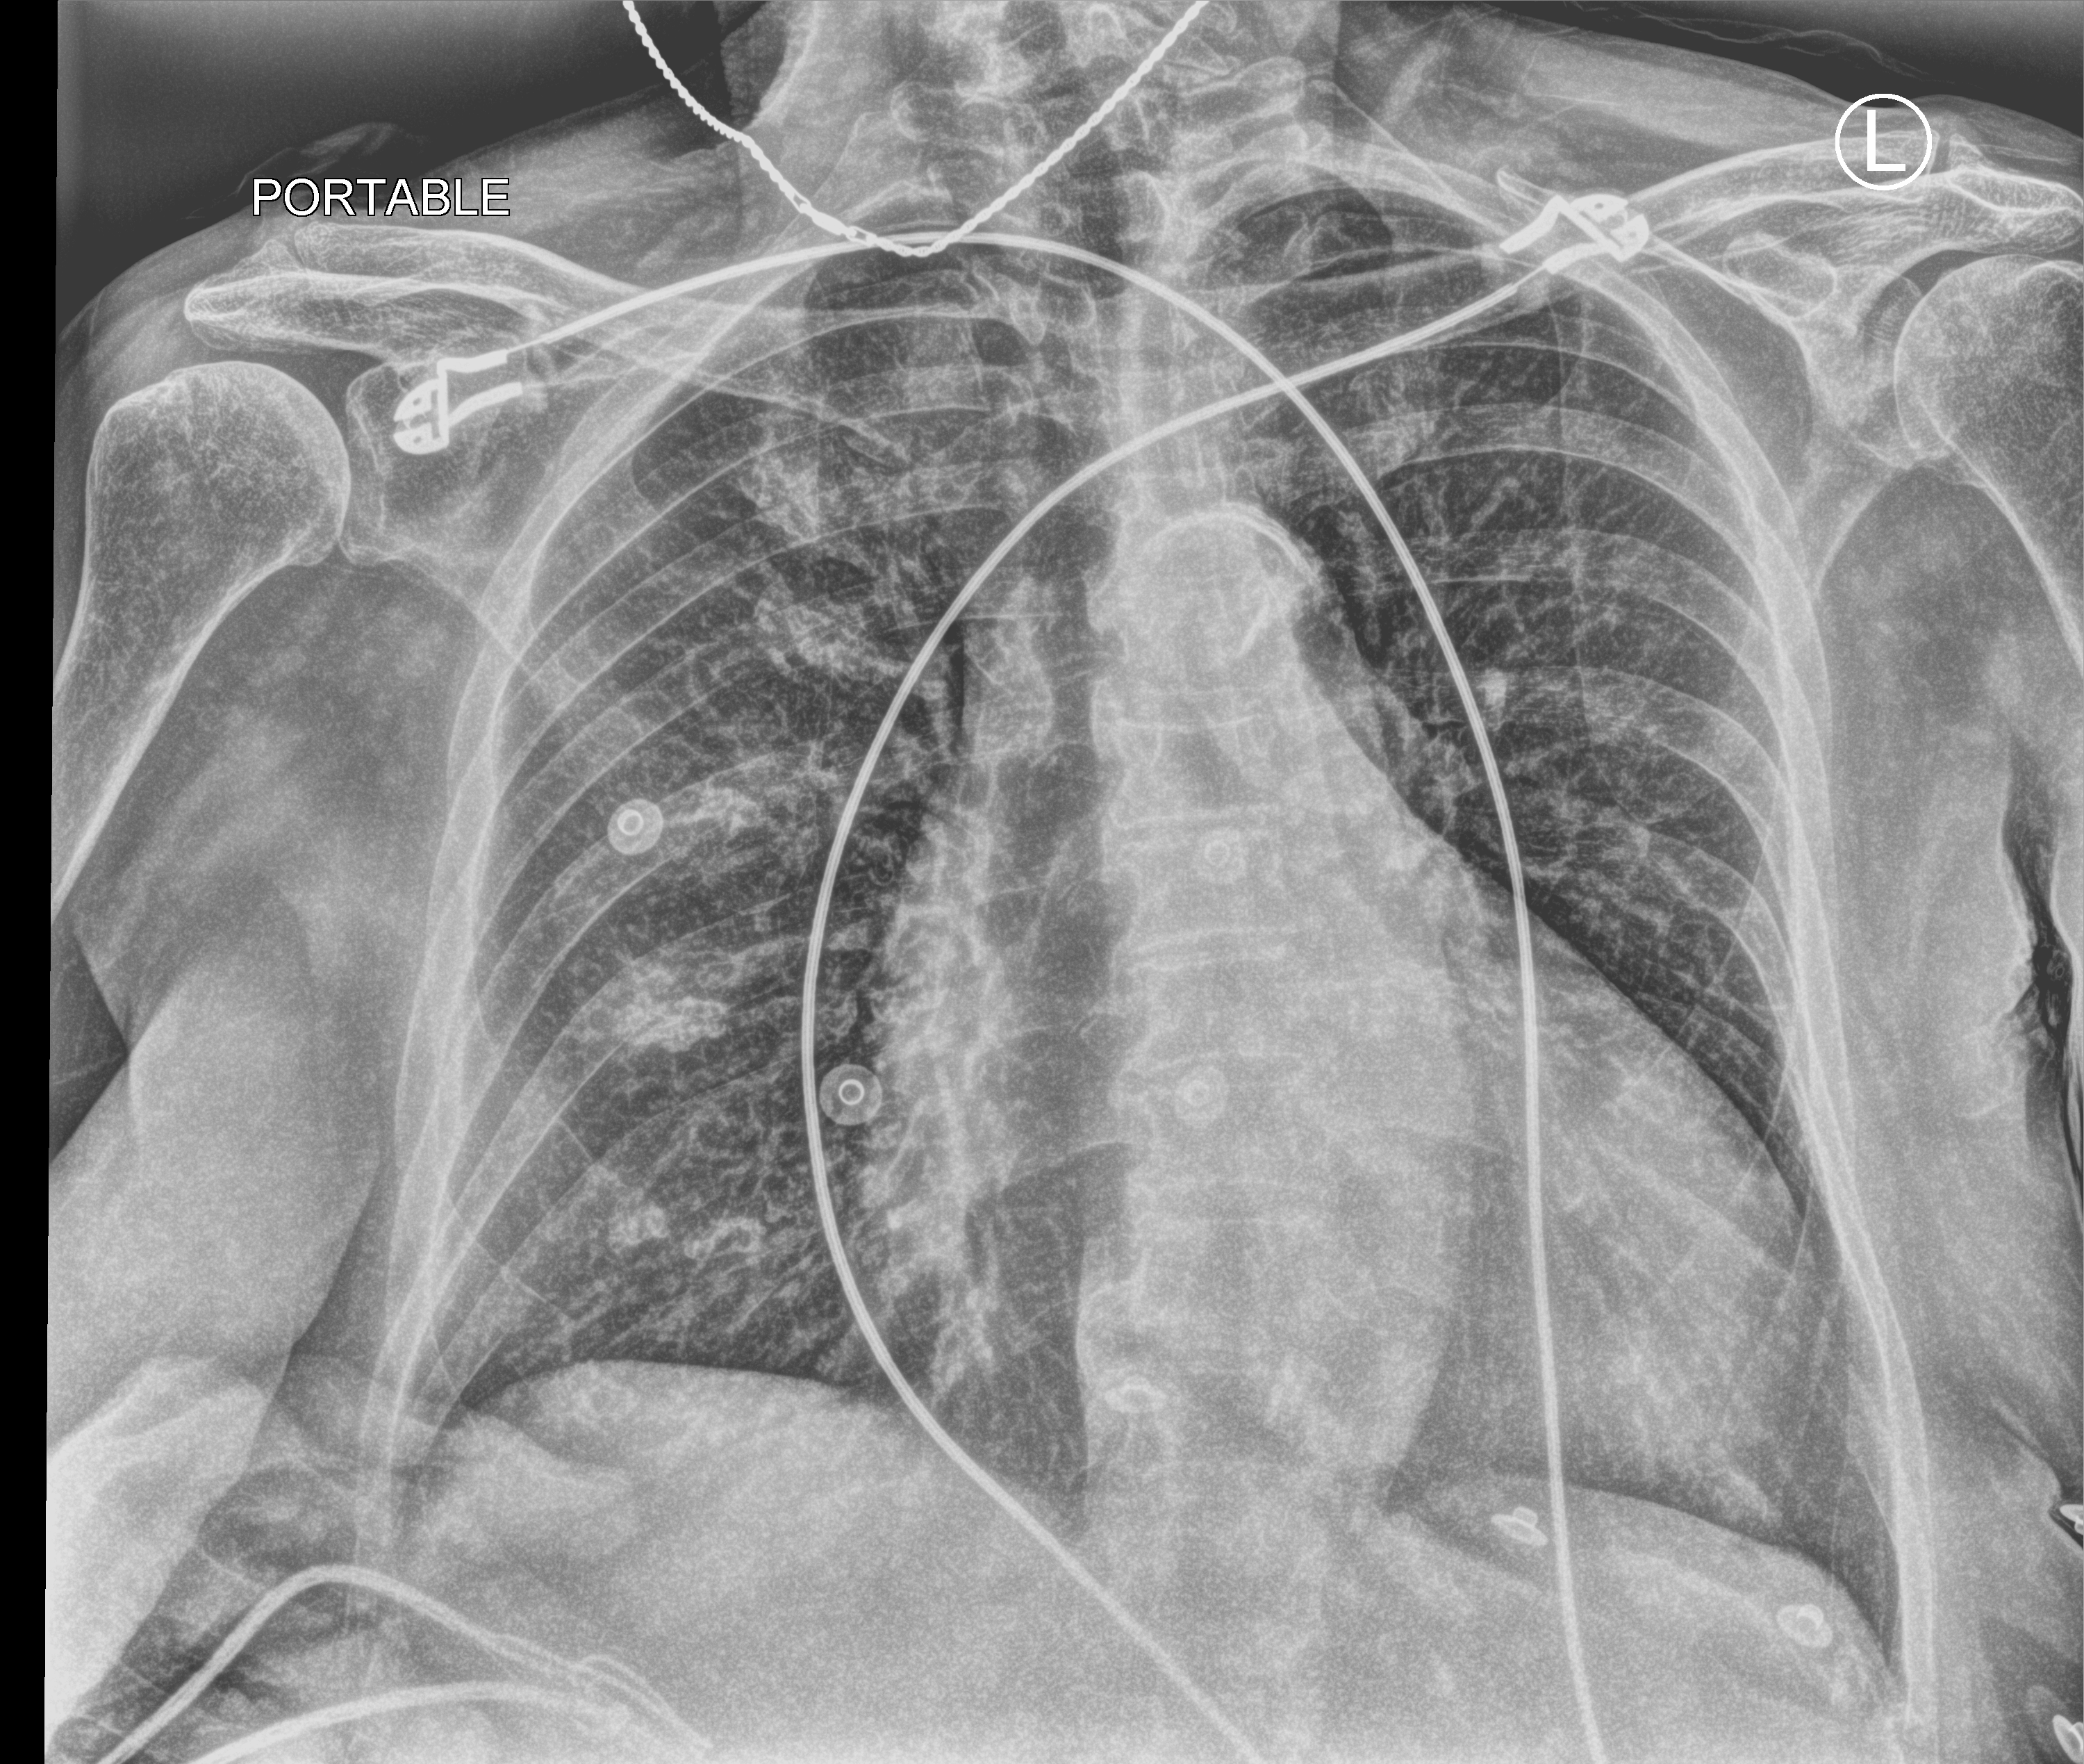
Bedside chest radiograph (computed radiography), anteroposterior (AP) projection. Female patient hospitalised with COVID-19, age 75–90 years.
Hospital-stay facts (about this admission, not read from this image; timing relative to this image not recorded): mechanically ventilated during this hospital stay: no.